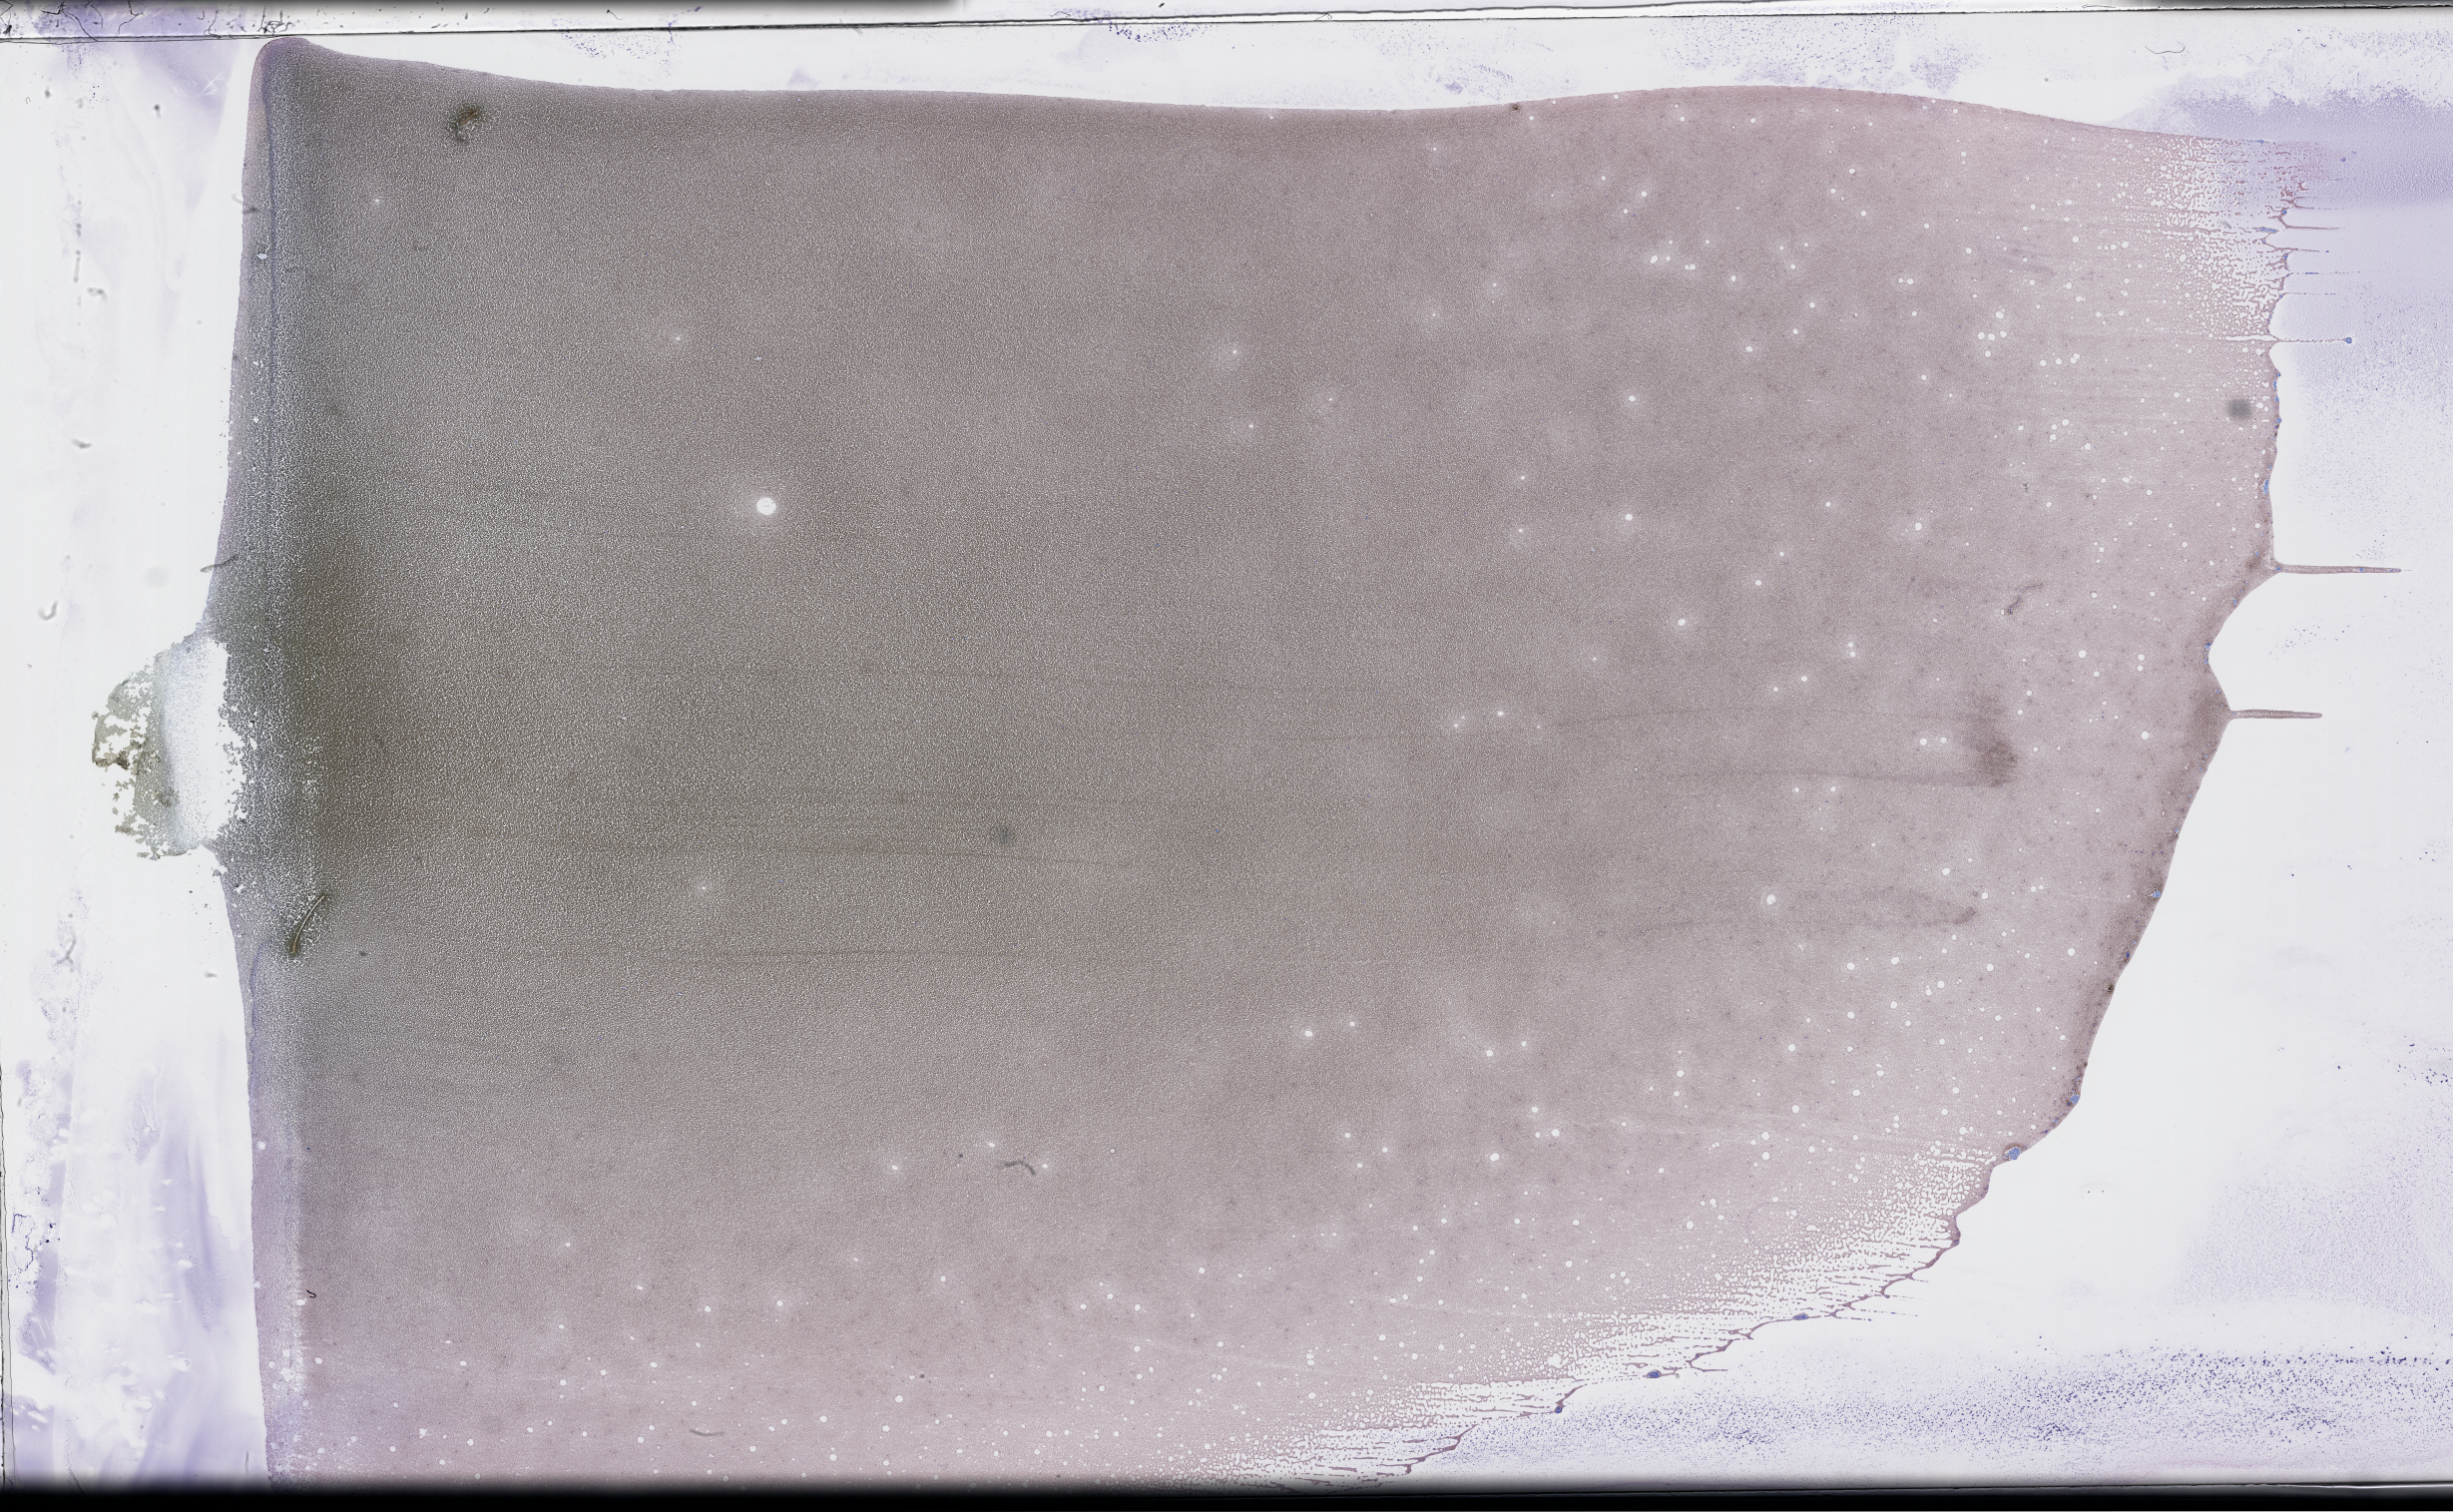
Wright-Giemsa-stained whole blood smear, whole-slide image, a low-resolution overview of the entire scanned area, about 39.7 x 24.5 mm. Smear from an EDTA sample. Collected on treatment. Patient: female.
* from a patient with: Plasma Cell Myeloma